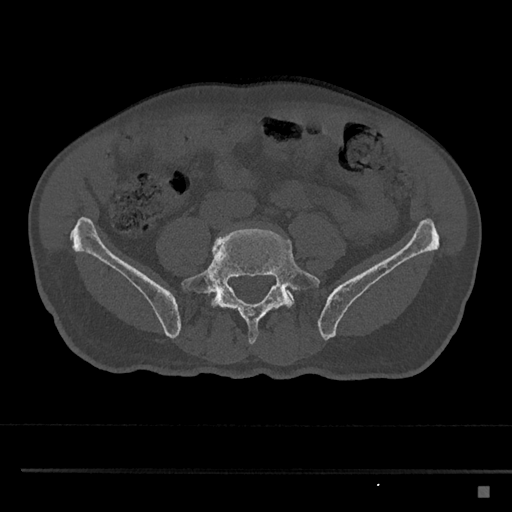
CT including the spine, one axial slice. 120 kVp. Bone window (W 1800 / L 400 HU). 512 × 512 image matrix, field of view 391 × 391 mm. Patient: male, 59 years. From the clinical record (not read from this slice): primary cancer: prostate.
Structures marked on this image (semi-automatic segmentation, software-assisted and operator-edited):
- L5 vertebra: bounding box <181,228,320,345> (left, top, right, bottom; pixels)